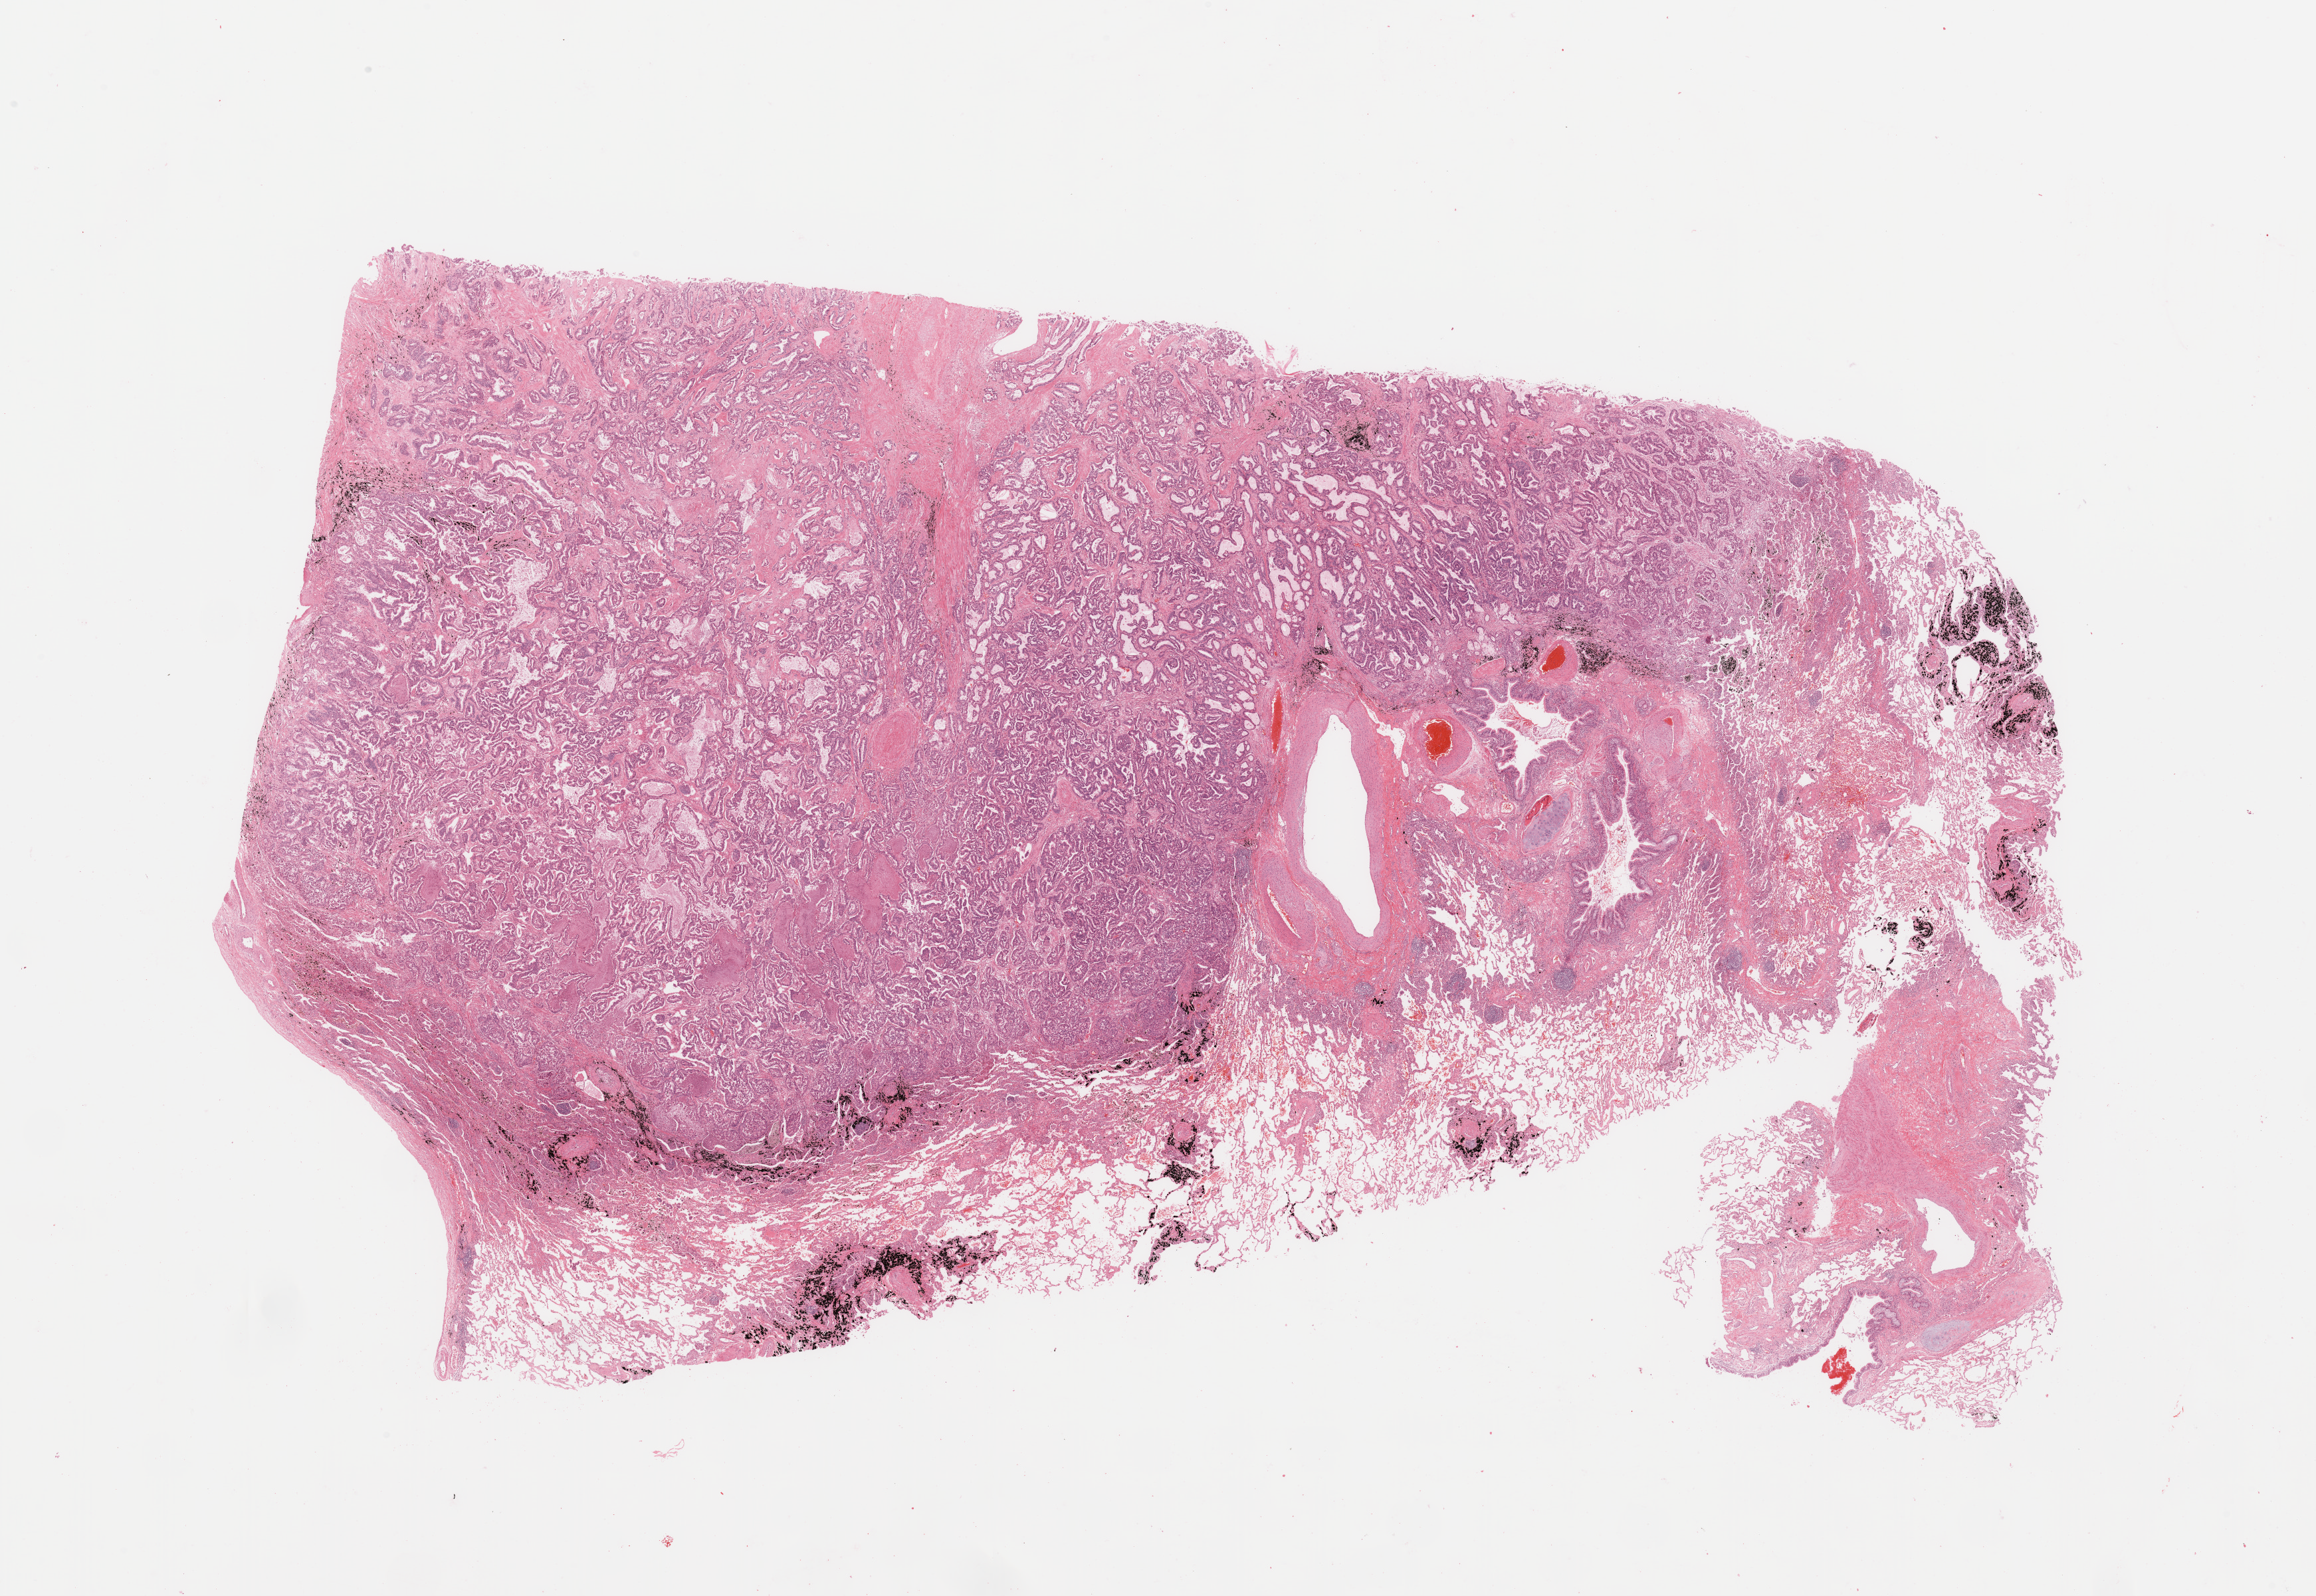
H&E whole-slide image, a low-resolution overview of the entire scanned area, about 27.6 x 19.0 mm (from a 20x scan). Tumour tissue sample, sampled site: lung. Patient: male, age 59 years. Histologic grade: G2 (moderately differentiated). Composition of this section per pathologist review: tumour nuclei 70%, necrosis 5%.
- diagnosis: Adenocarcinoma, NOS
- primary tumour site (as recorded): left upper lobe
- AJCC pathologic stage: IB